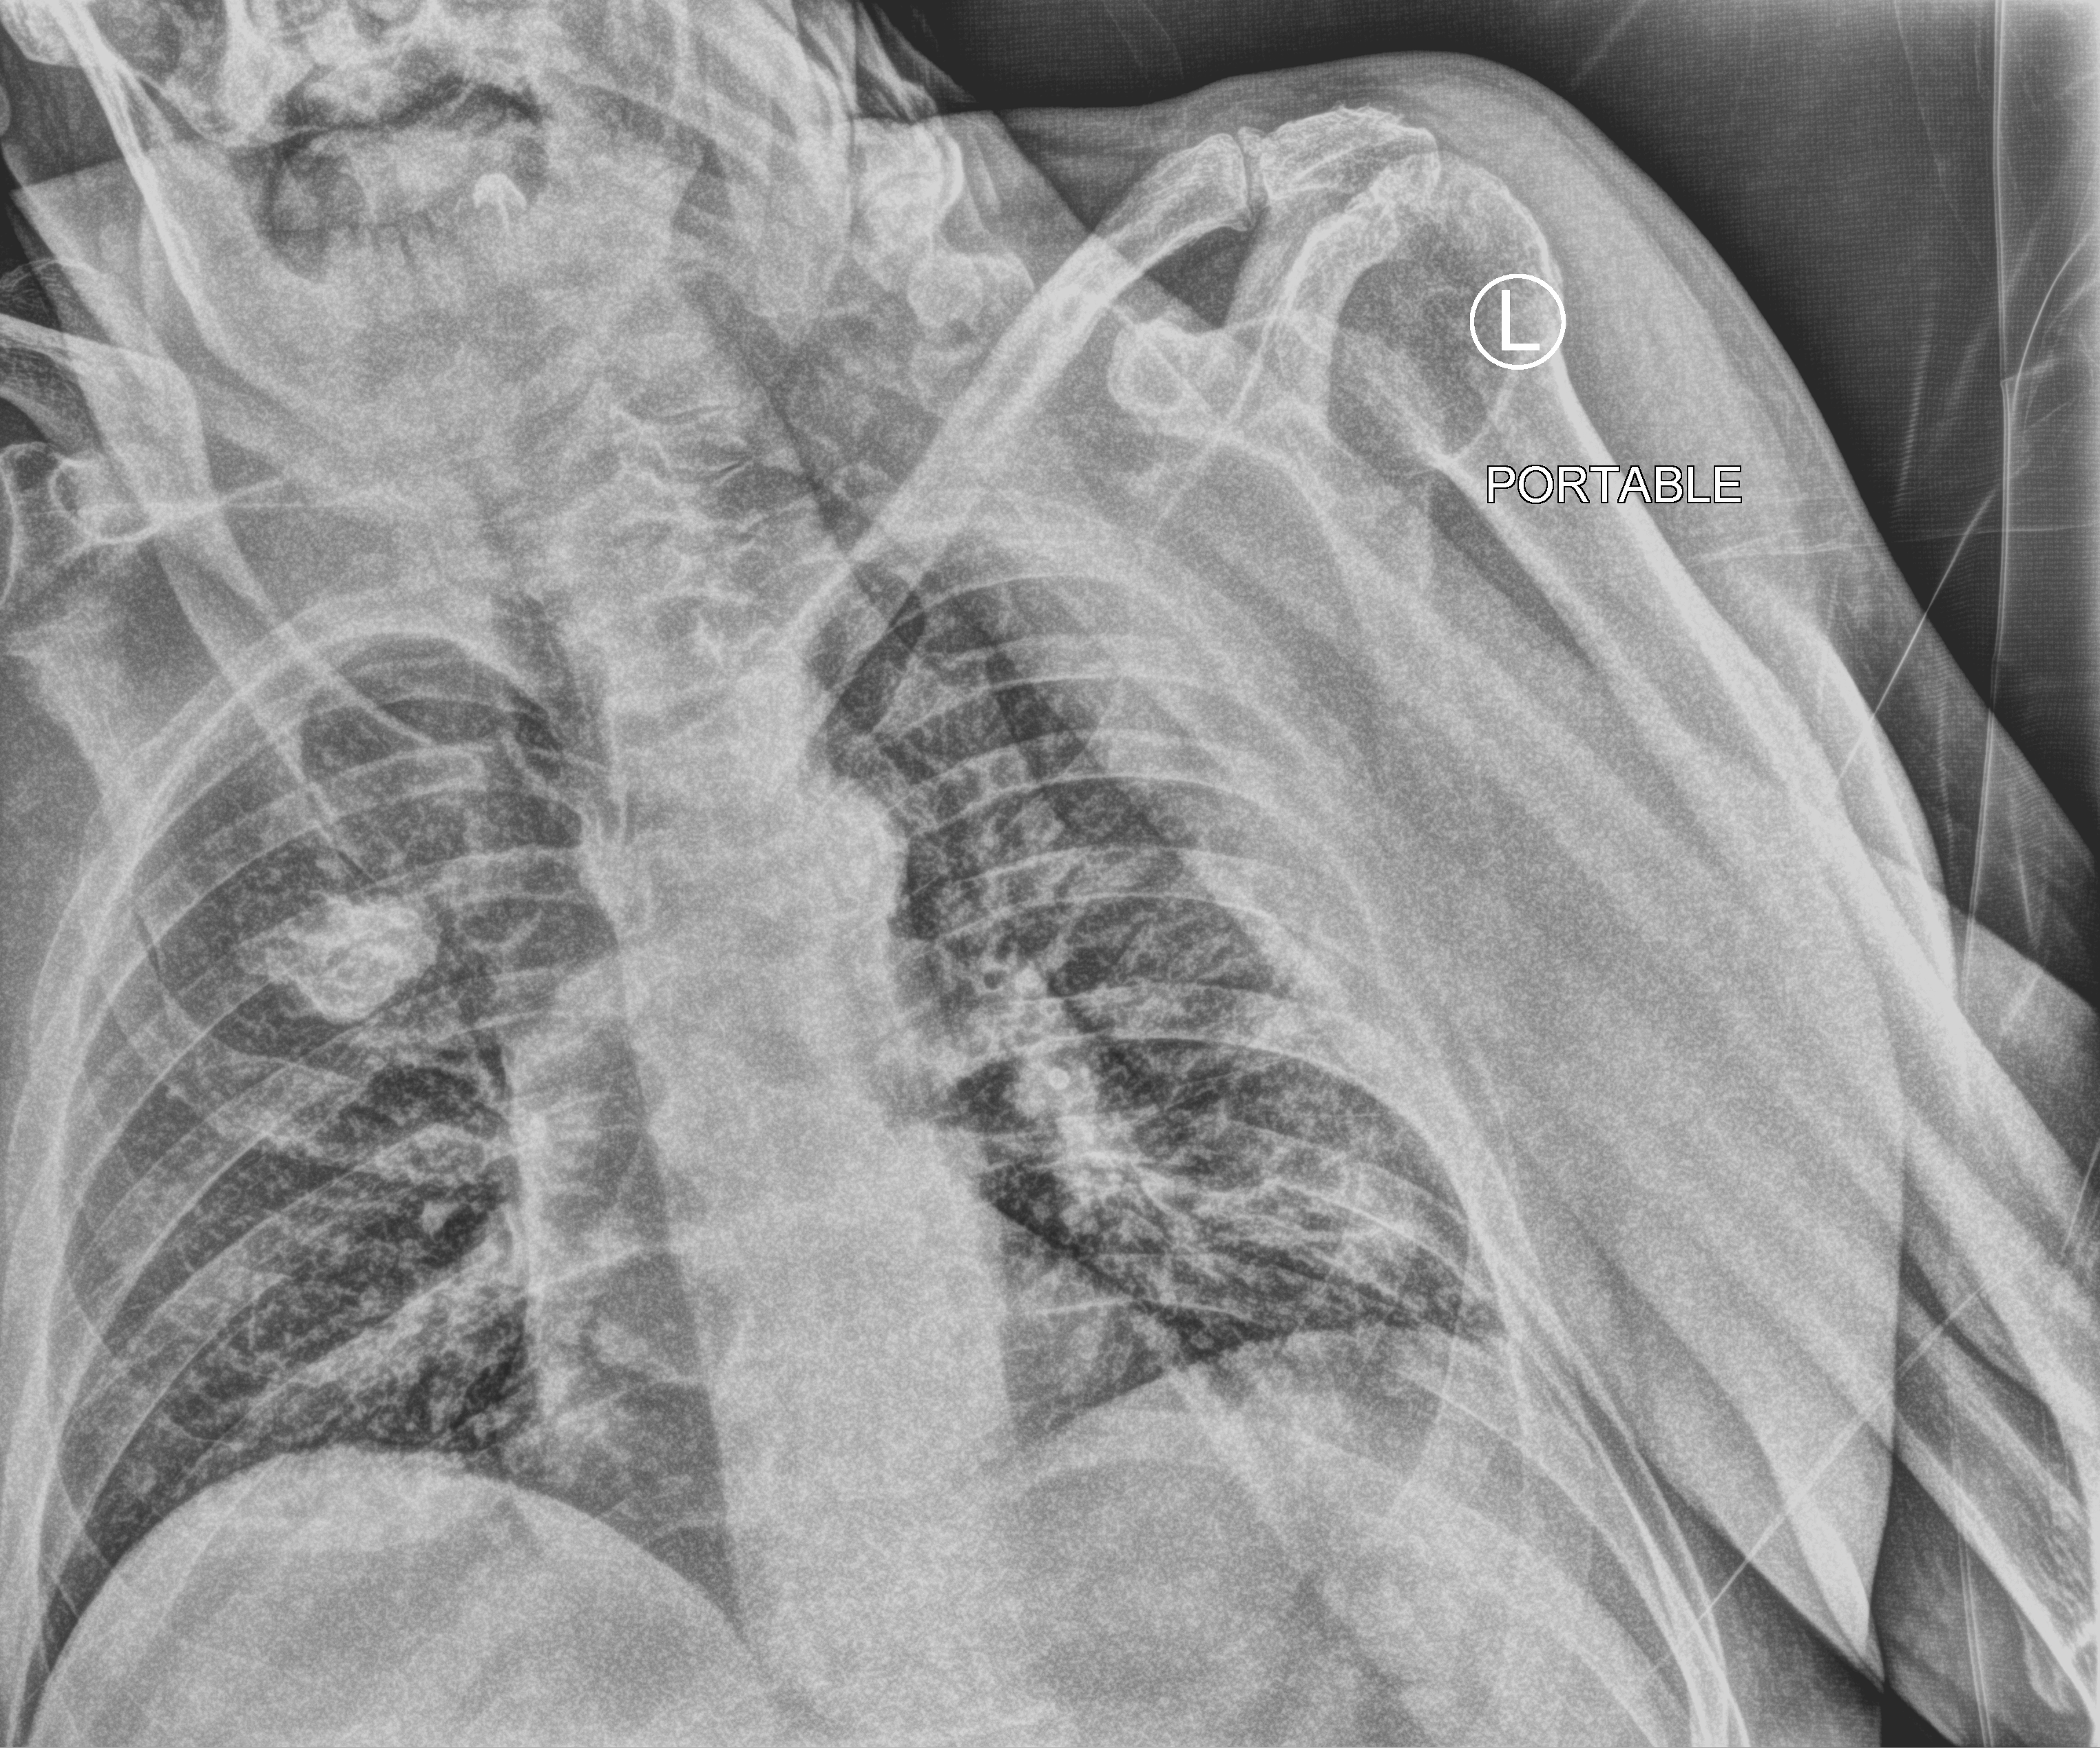
Chest X-ray (portable); anteroposterior (AP) projection. Patient hospitalised with COVID-19; male, aged 75–90 years.
From the hospital-stay record, not from the radiograph (when in the stay this image was taken is not recorded): length of hospital stay: 32 days; mechanically ventilated during this hospital stay: no.